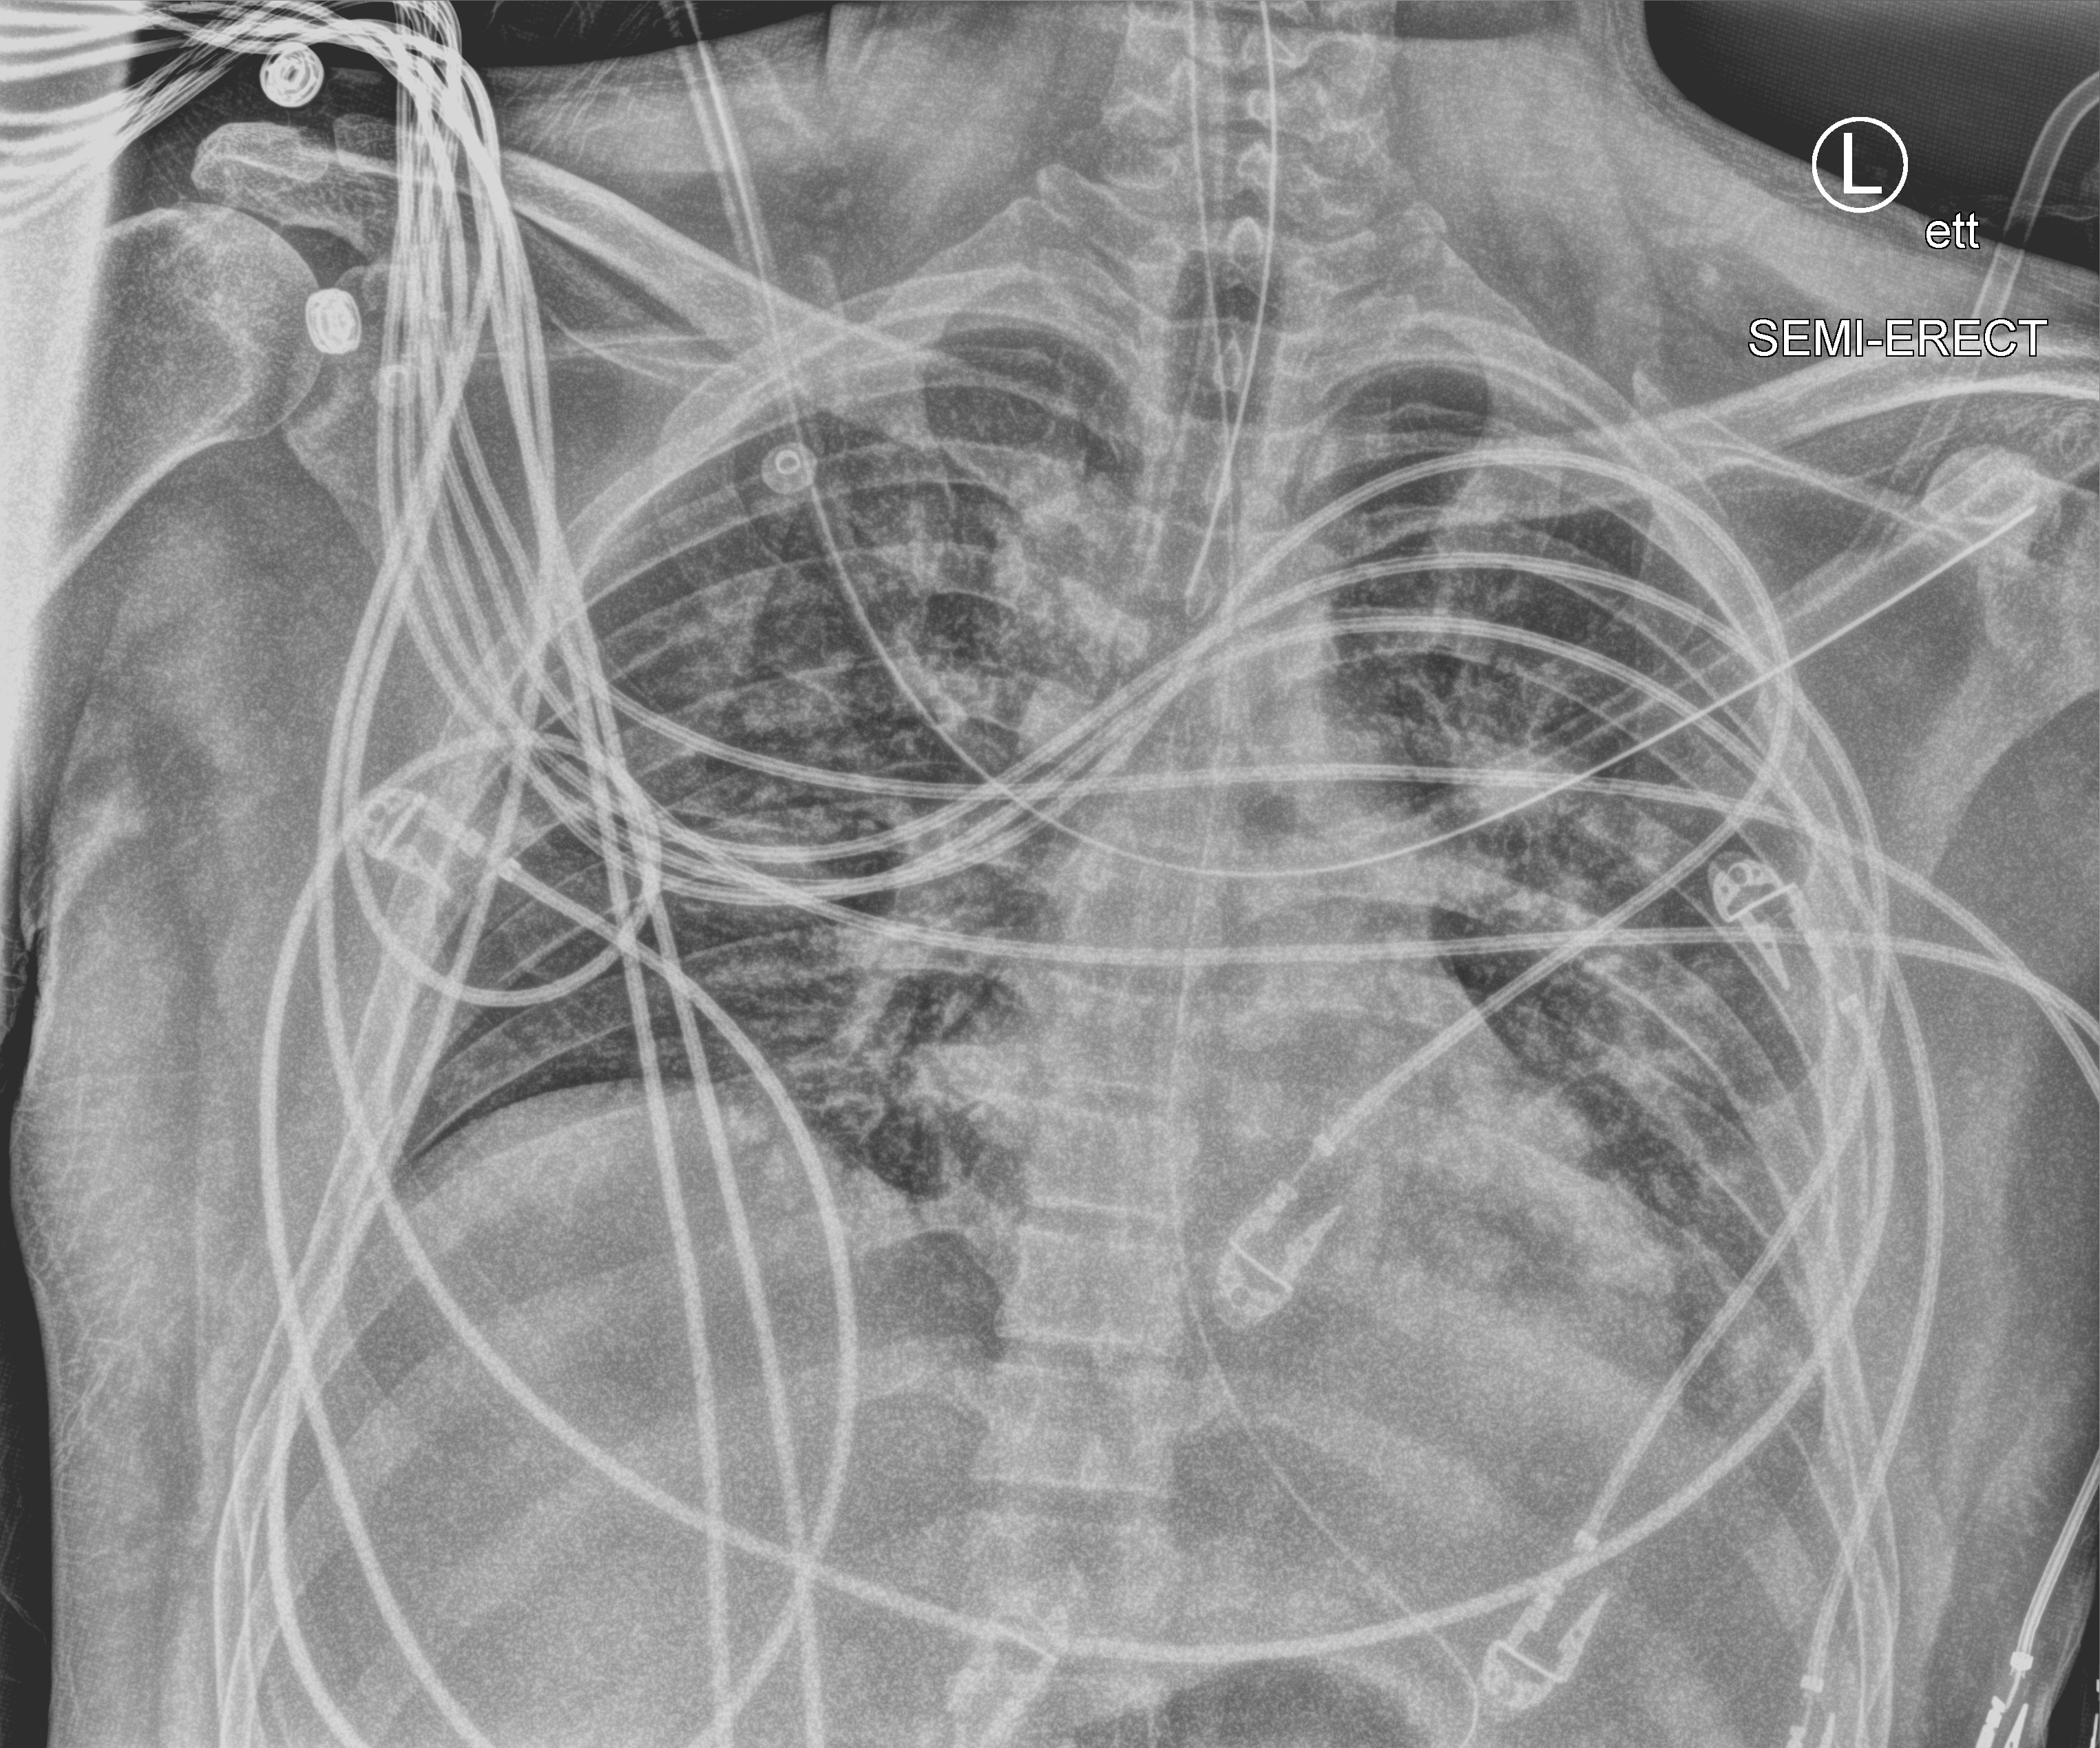
Chest X-ray (portable), anteroposterior (AP) projection. Adult patient hospitalised with COVID-19, age 18–59 years.
Hospital-stay facts (about this admission, not read from this image; timing relative to this image not recorded): other chronic lung disease (admission record): no; smoking status (admission record): never; mechanically ventilated during this hospital stay: yes.